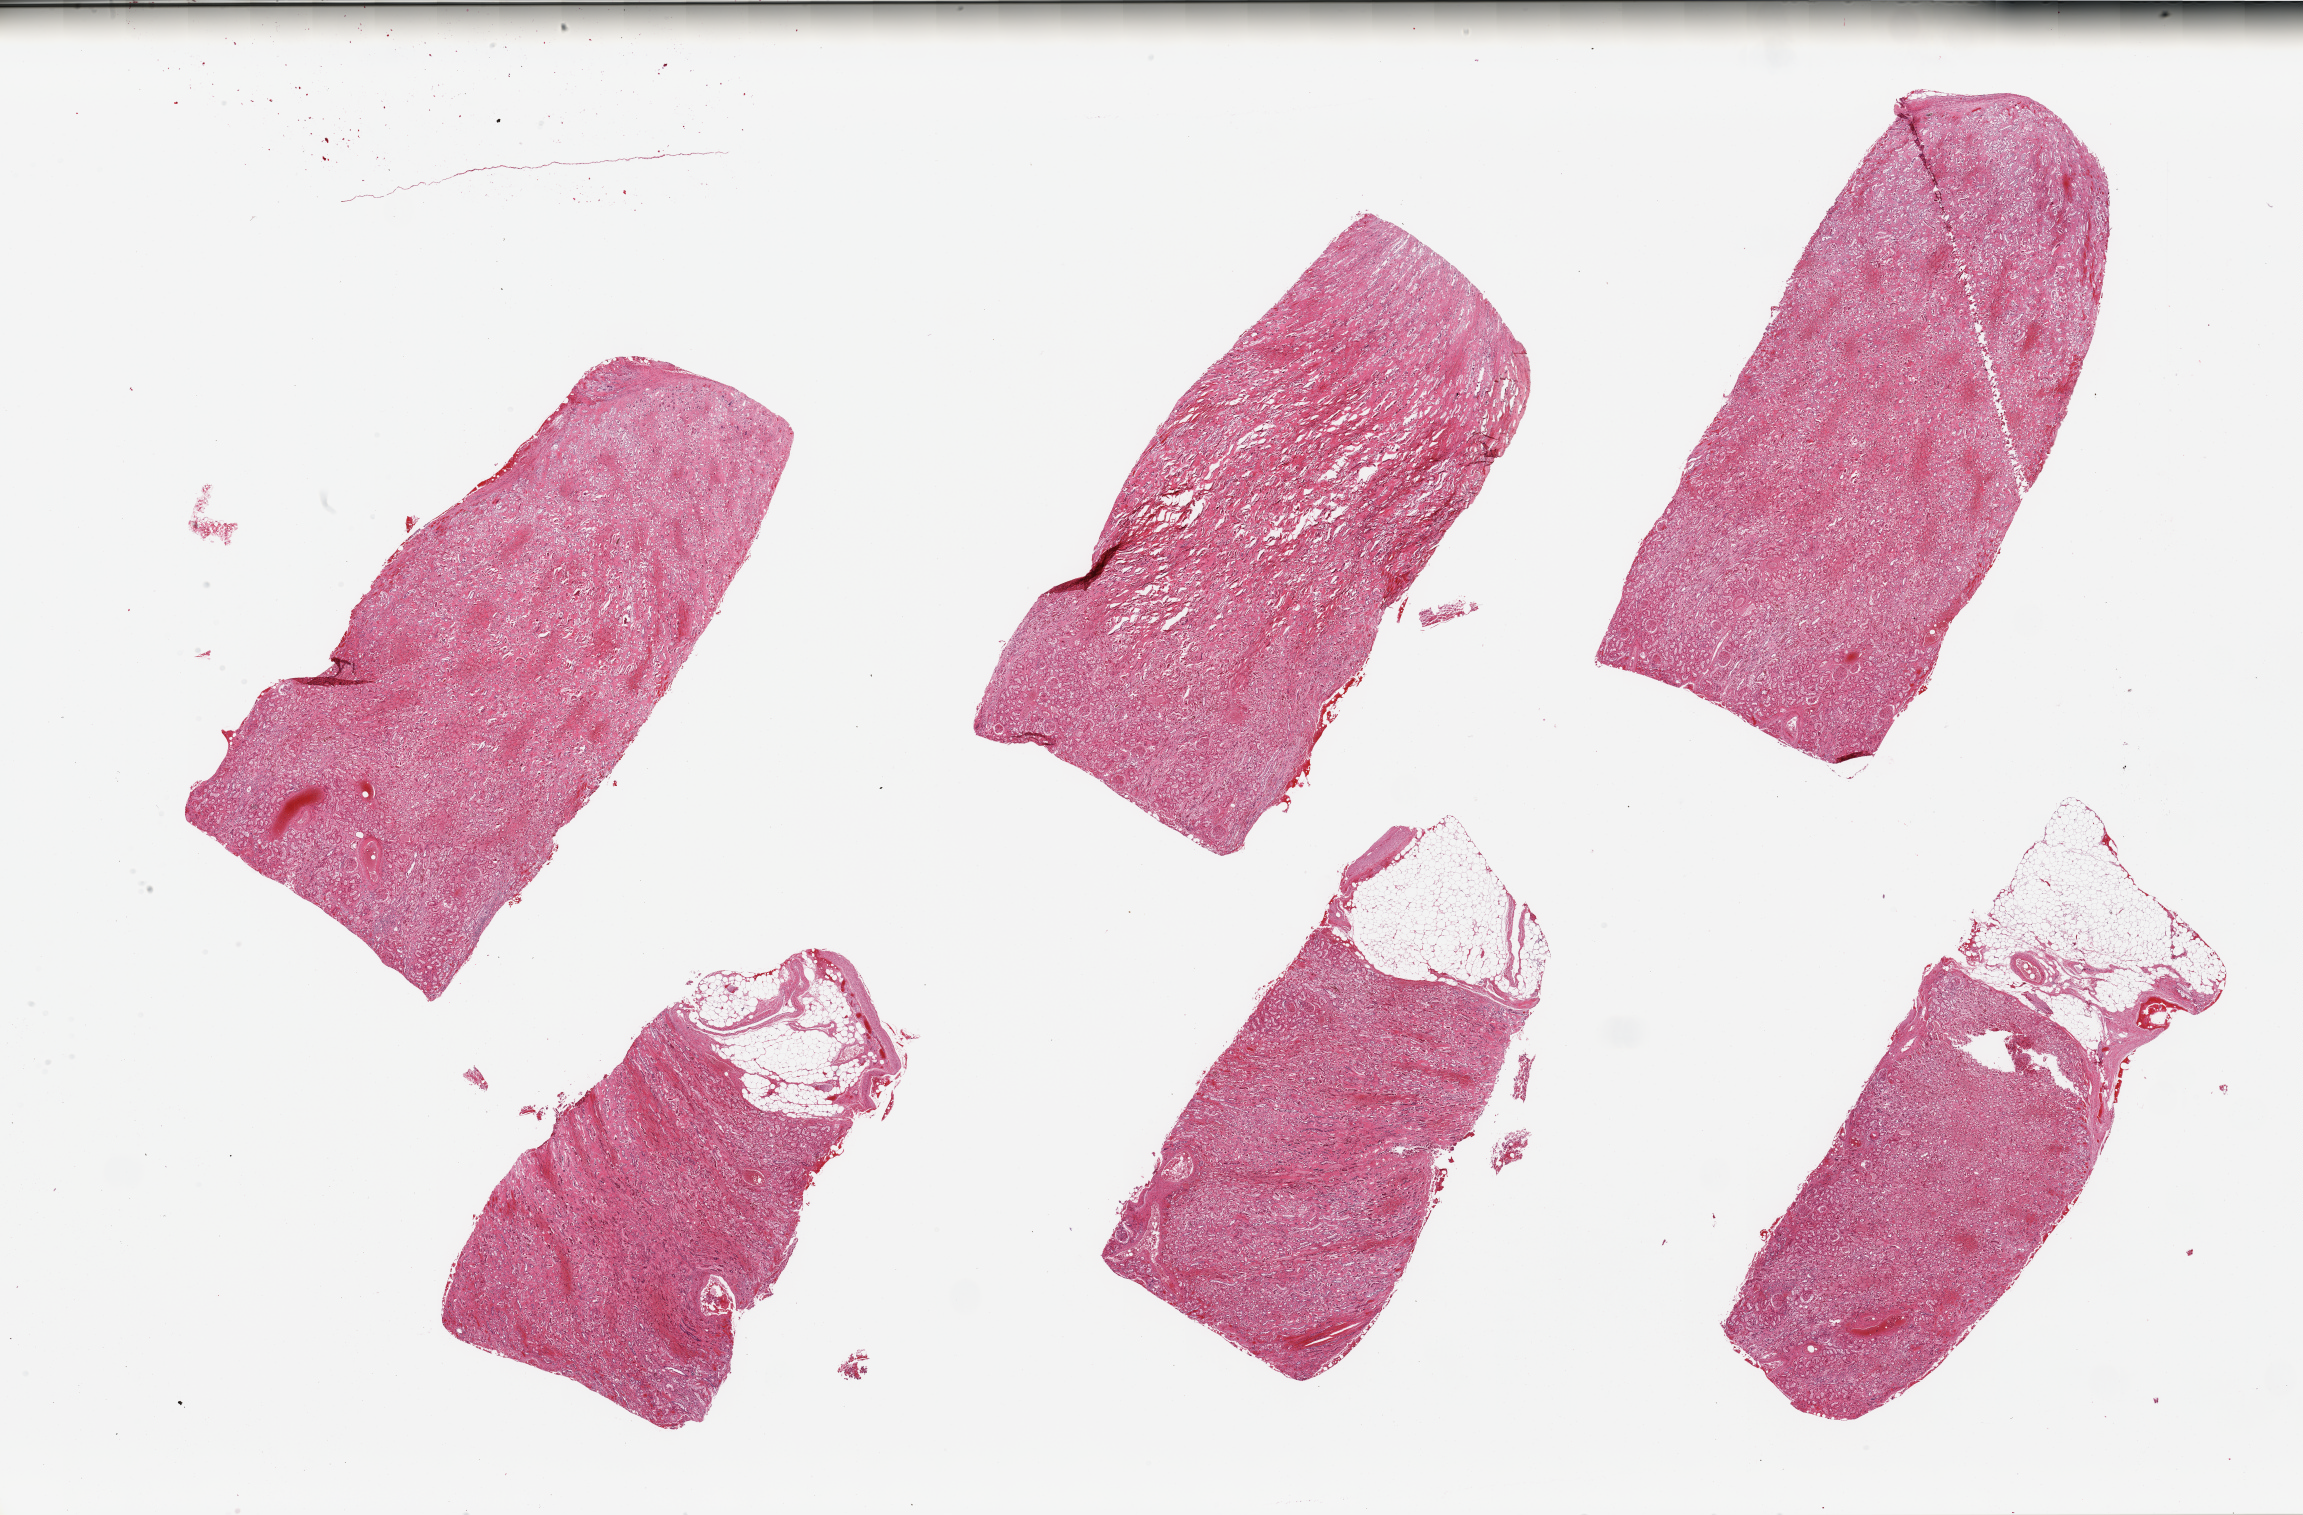
Digitized hematoxylin and eosin (H&E)-stained section — low-resolution overview of the scanned area, about 36.4 x 24.0 mm, PAXgene-fixed, paraffin-embedded tissue, sampled site (target tissue): renal cortex, tissue donor sample. Male donor.
Pathologist's review note for this sample: 6 pieces; significant component of fat and medulla.